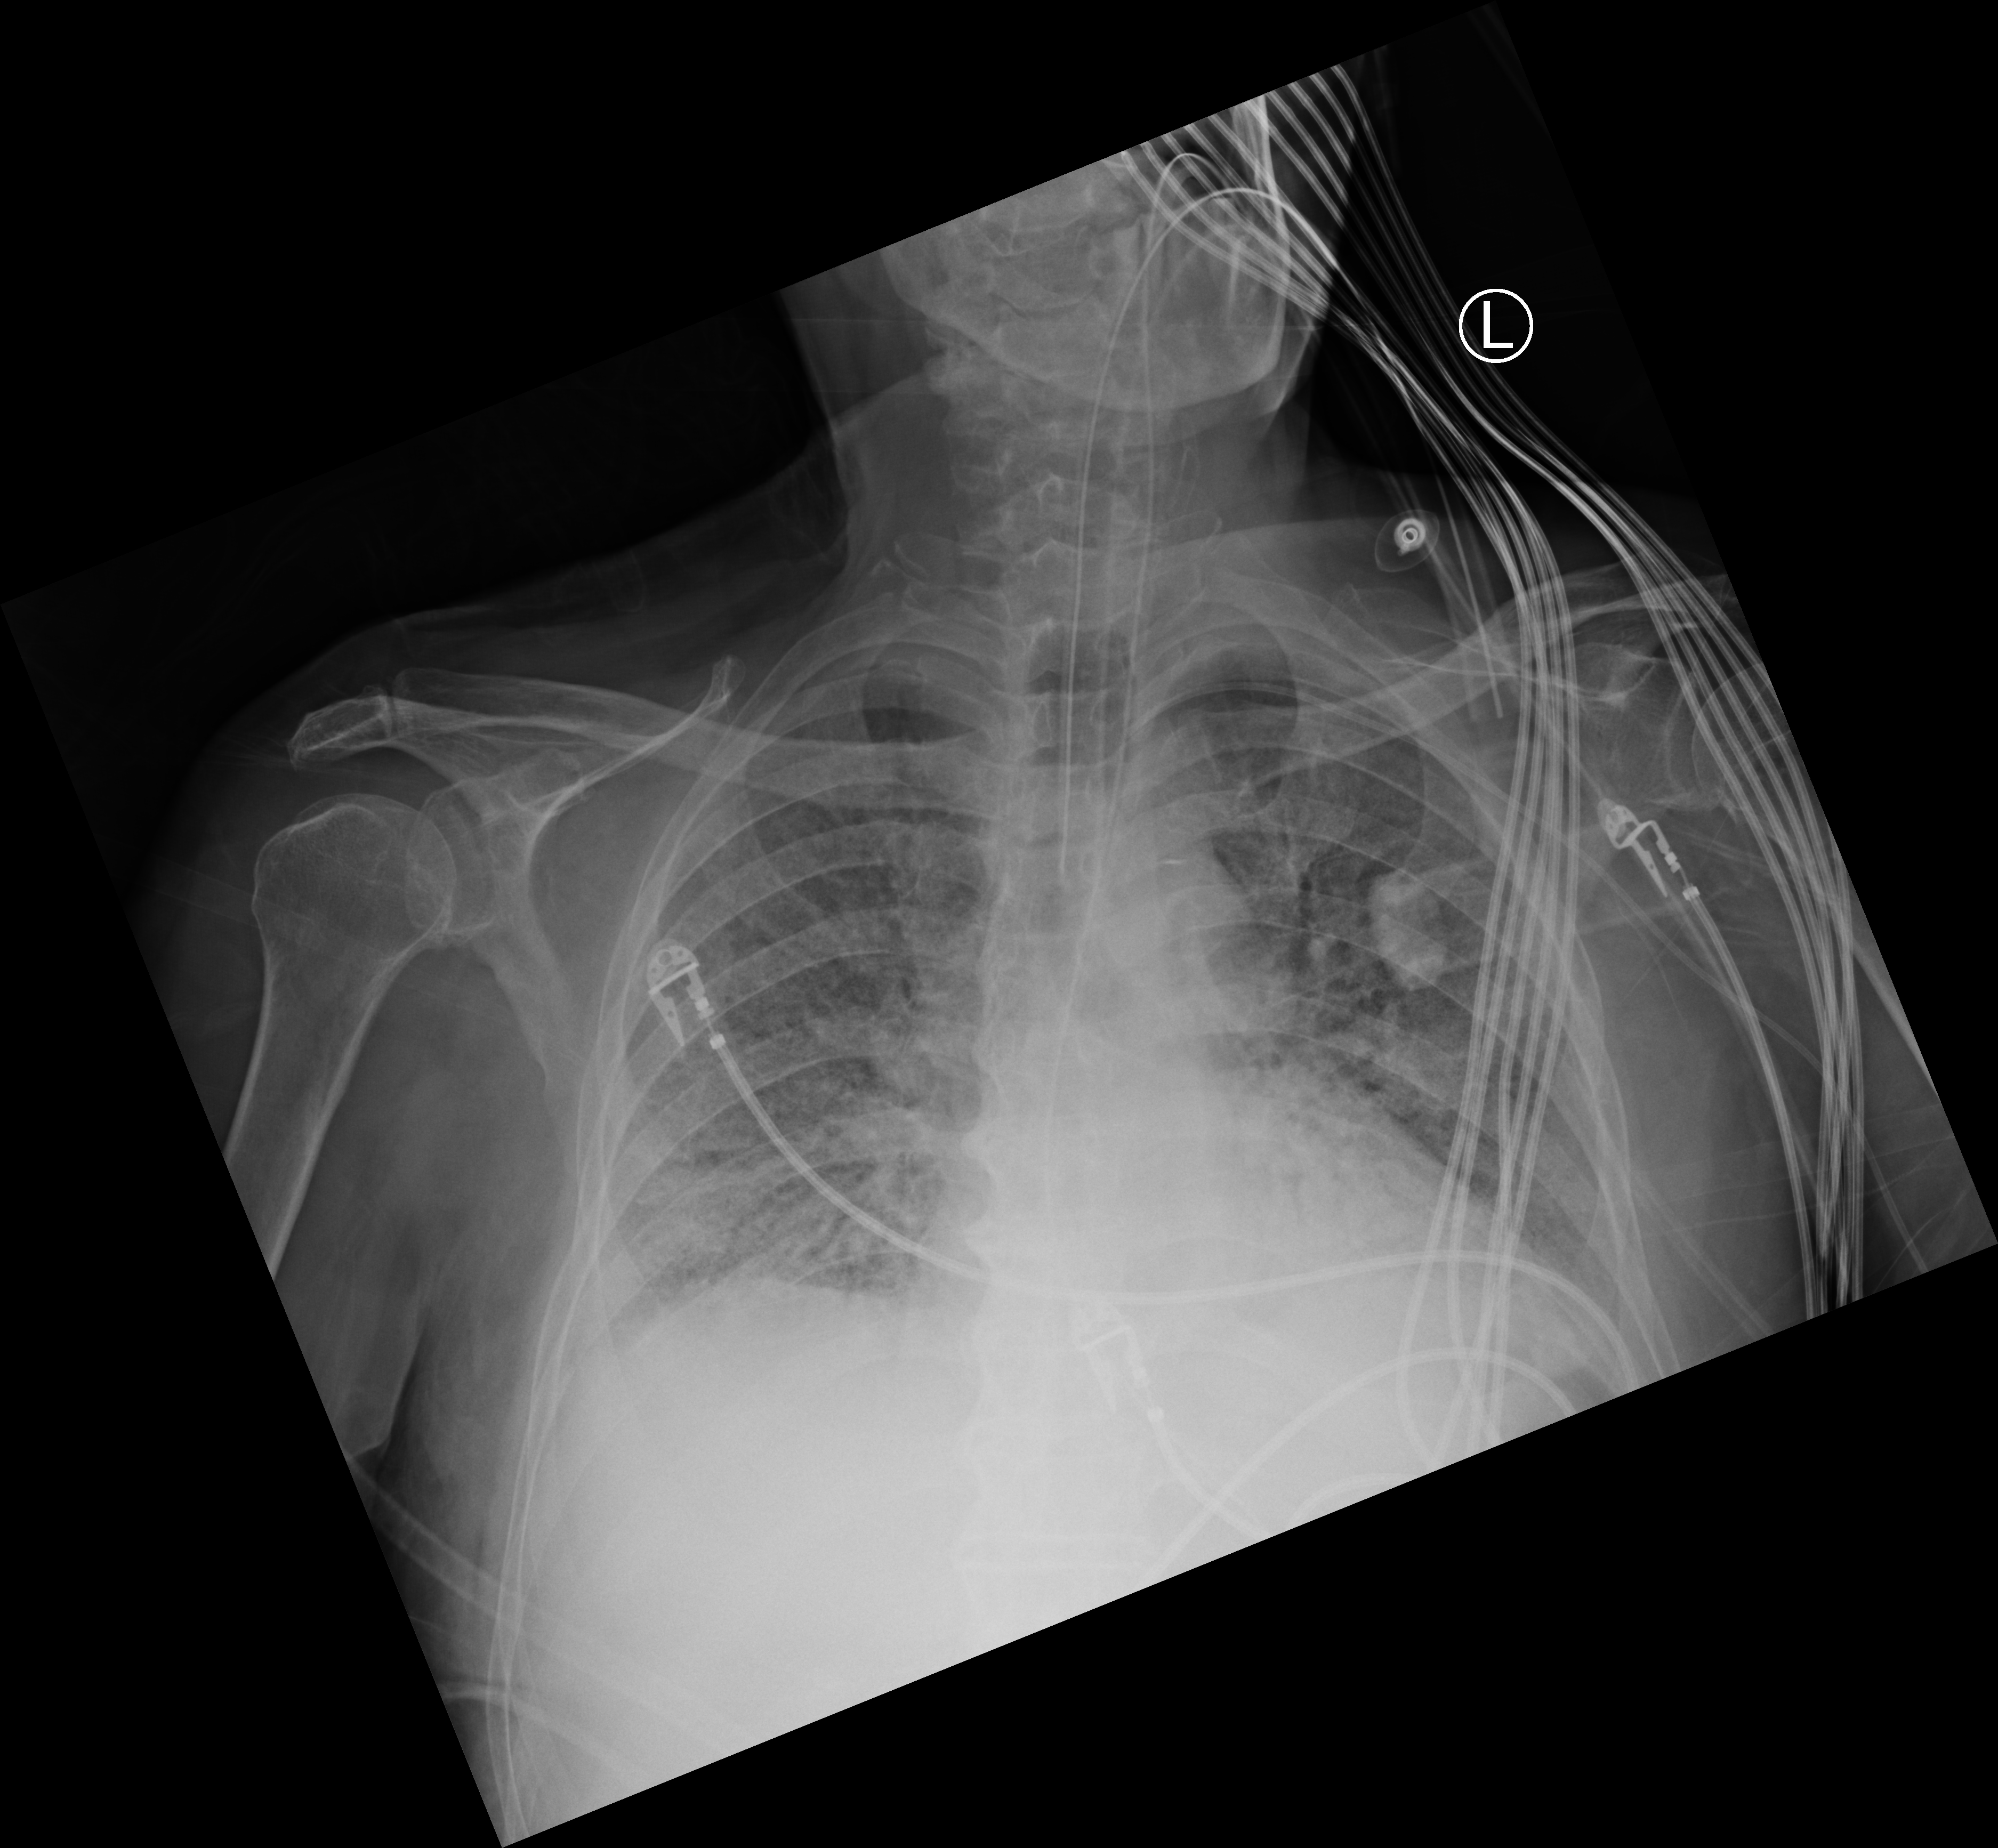
Chest X-ray (portable); anteroposterior (AP) projection. Male patient hospitalised with COVID-19, age 75–90 years.
From the hospital-stay record, not from the radiograph (when in the stay this image was taken is not recorded): COPD (admission record): no; admitted to intensive care during this hospital stay: yes; hypertension (admission record): yes.